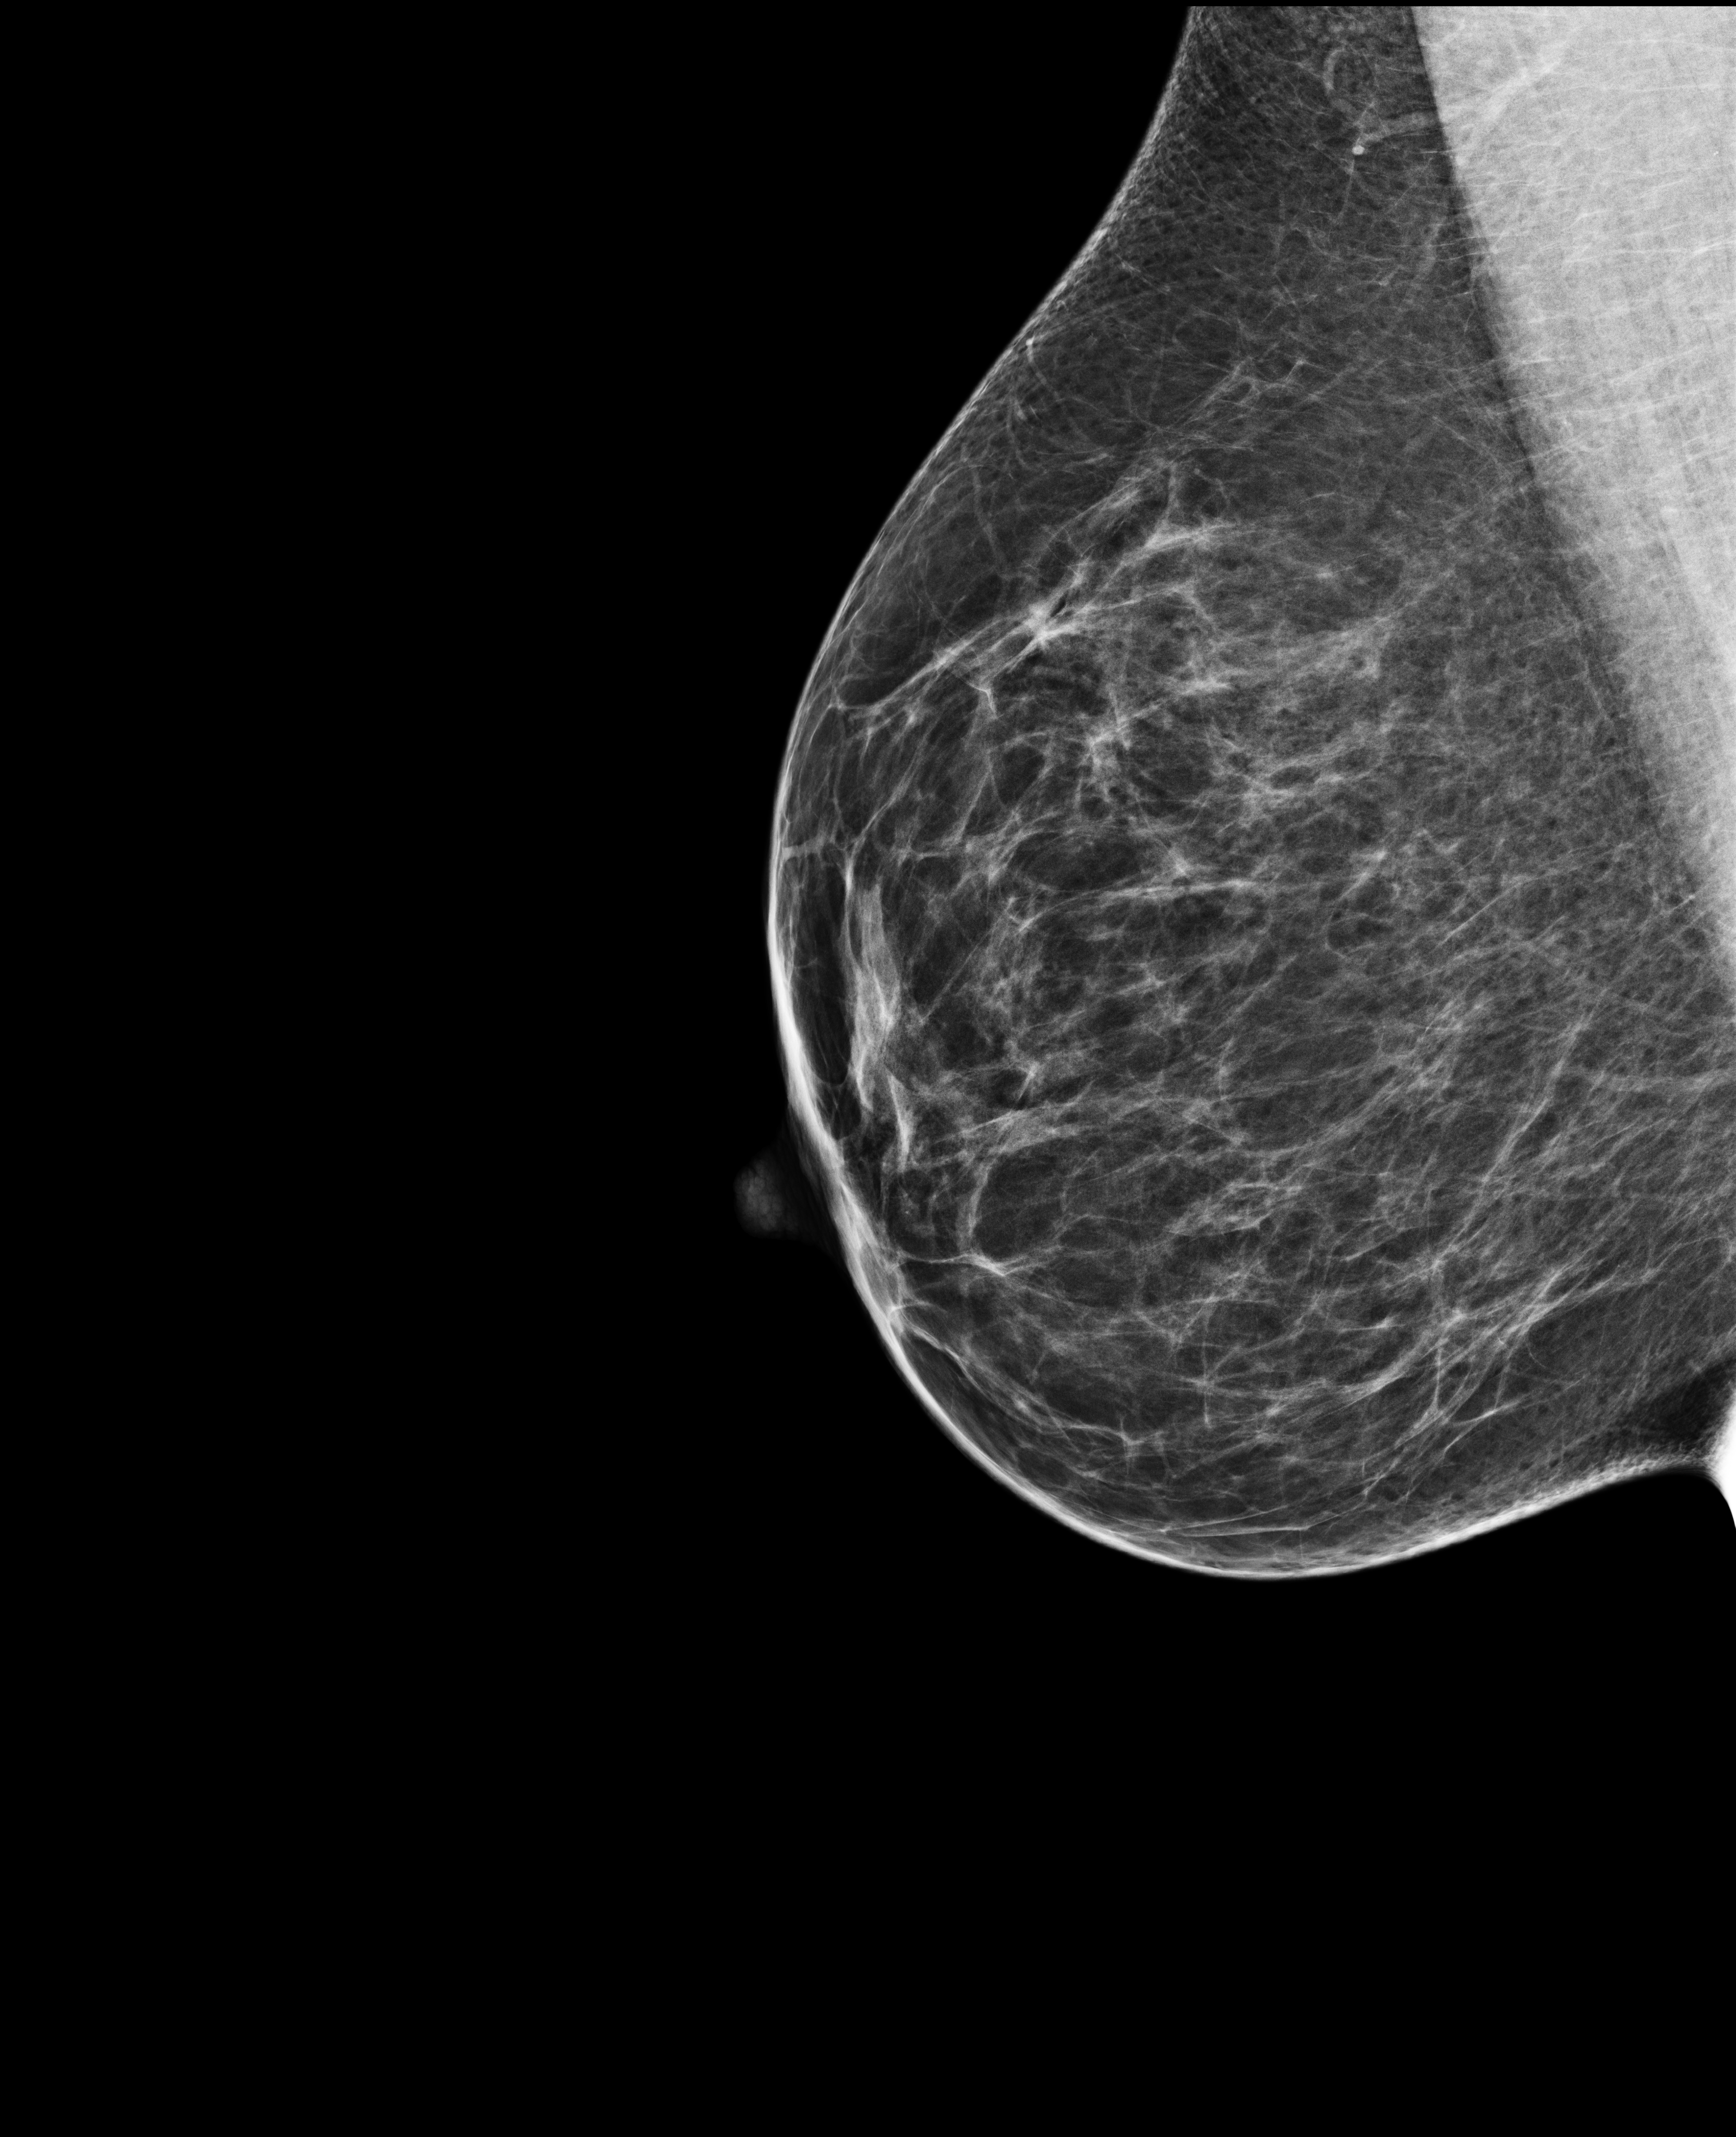
Full-field digital mammogram (FFDM); right breast; mediolateral oblique (MLO) view; annual screening mammography examination. Female patient, age 41 years.
- breast density at the screening exam (both breasts): heterogeneously dense (BI-RADS density category c)
- final BI-RADS category for the screening round (tomosynthesis exam, both breasts): category 1
- recall: no recall after this screen